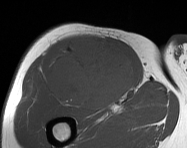
MRI of an extremity soft-tissue mass, one axial slice; slice 95 of 114 in the series (ordered by position); MR volume resampled by the dataset authors to the PET/CT grid (not the native acquisition matrix); 187 × 148 image matrix, field of view 183 × 145 mm. Male patient. From the clinical record (not read from this slice): histological type: pleiomorphic leiomyosarcoma; grade: intermediate; site of the primary tumour: right thigh.
Annotated regions visible in this slice (expert contour drawn on MRI and transferred to this co-registered scan by the dataset authors):
- gross tumour volume including surrounding oedema: bounding box (x1, y1, x2, y2) in pixels: (47, 36, 135, 108)
- gross tumour volume (mass): (48, 36, 135, 108)